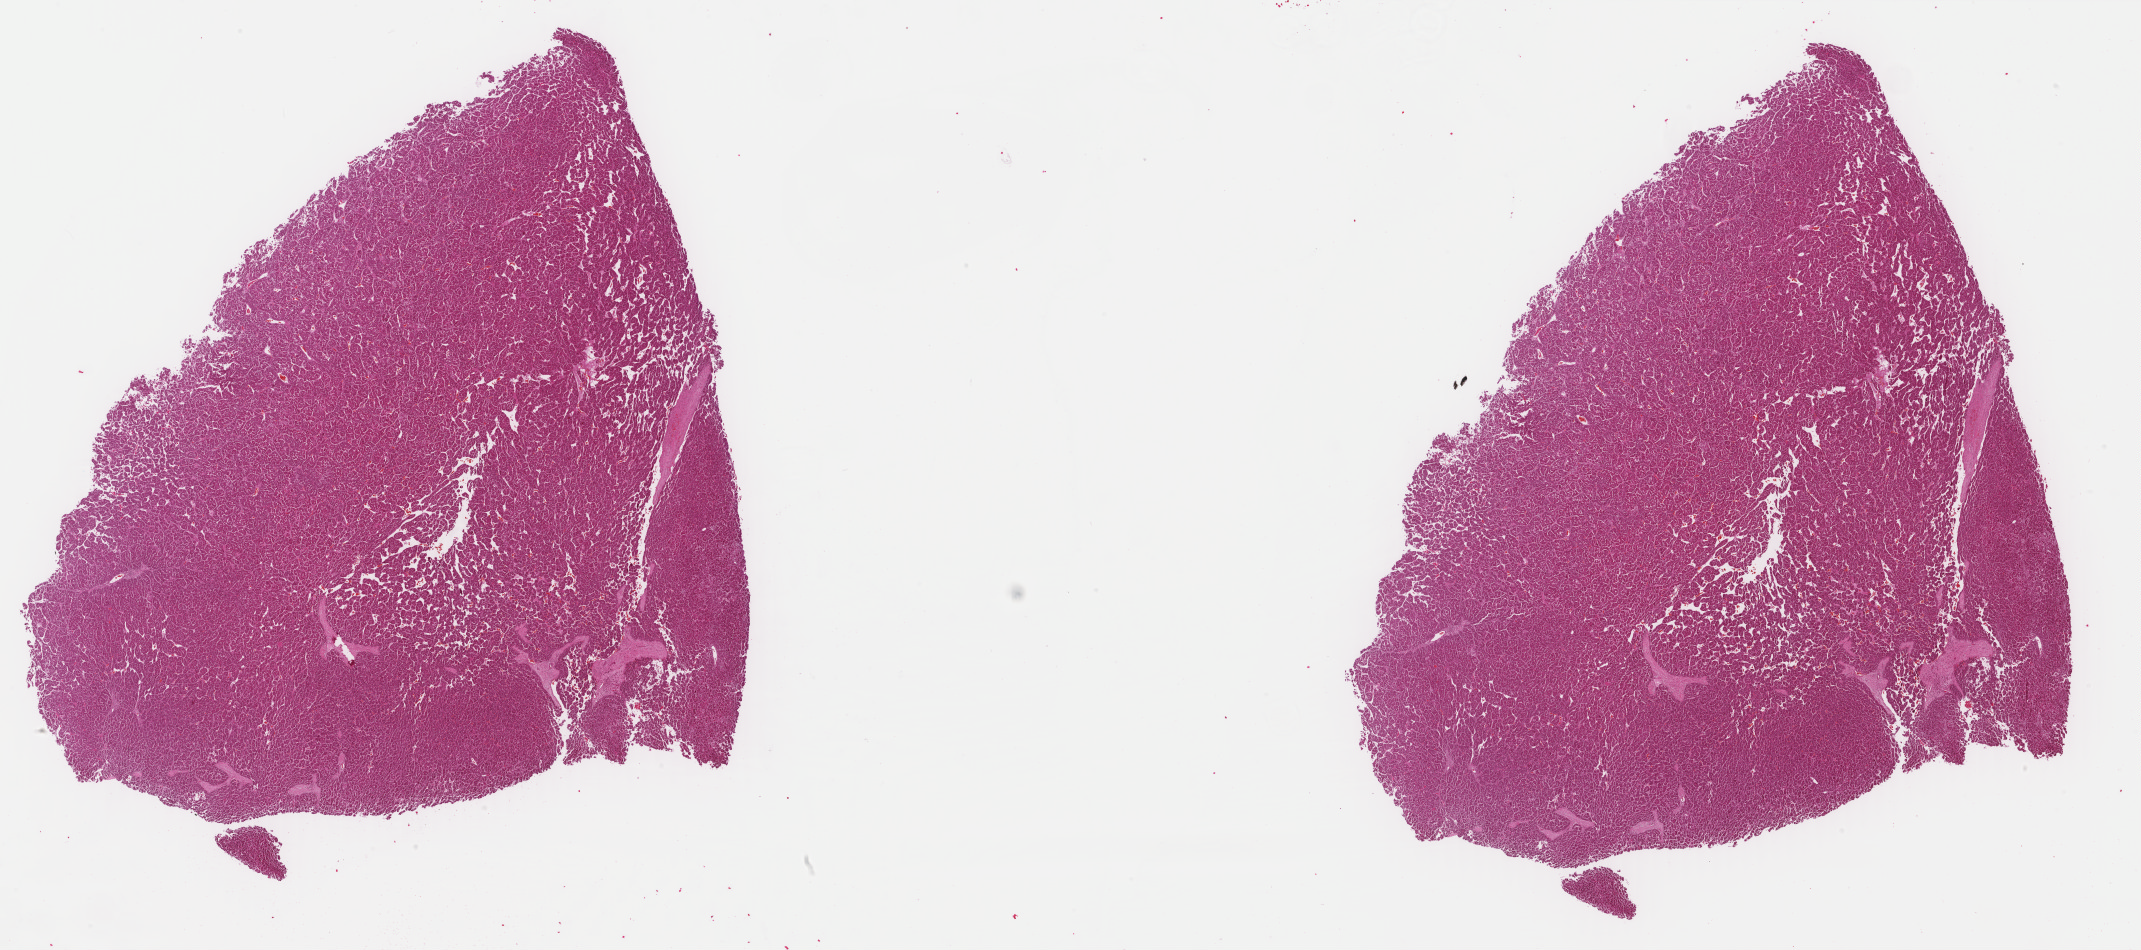
H&E-stained whole-slide image — shown as a low-resolution overview of the whole scanned area (about 34.0 x 15.1 mm). Formalin-fixed paraffin-embedded (FFPE) diagnostic section. Sample: primary tumour, liver. Male patient; age at initial diagnosis 50 years. Histologic grade: G3 (poorly differentiated).
* pathologic diagnosis: Hepatocellular carcinoma, NOS